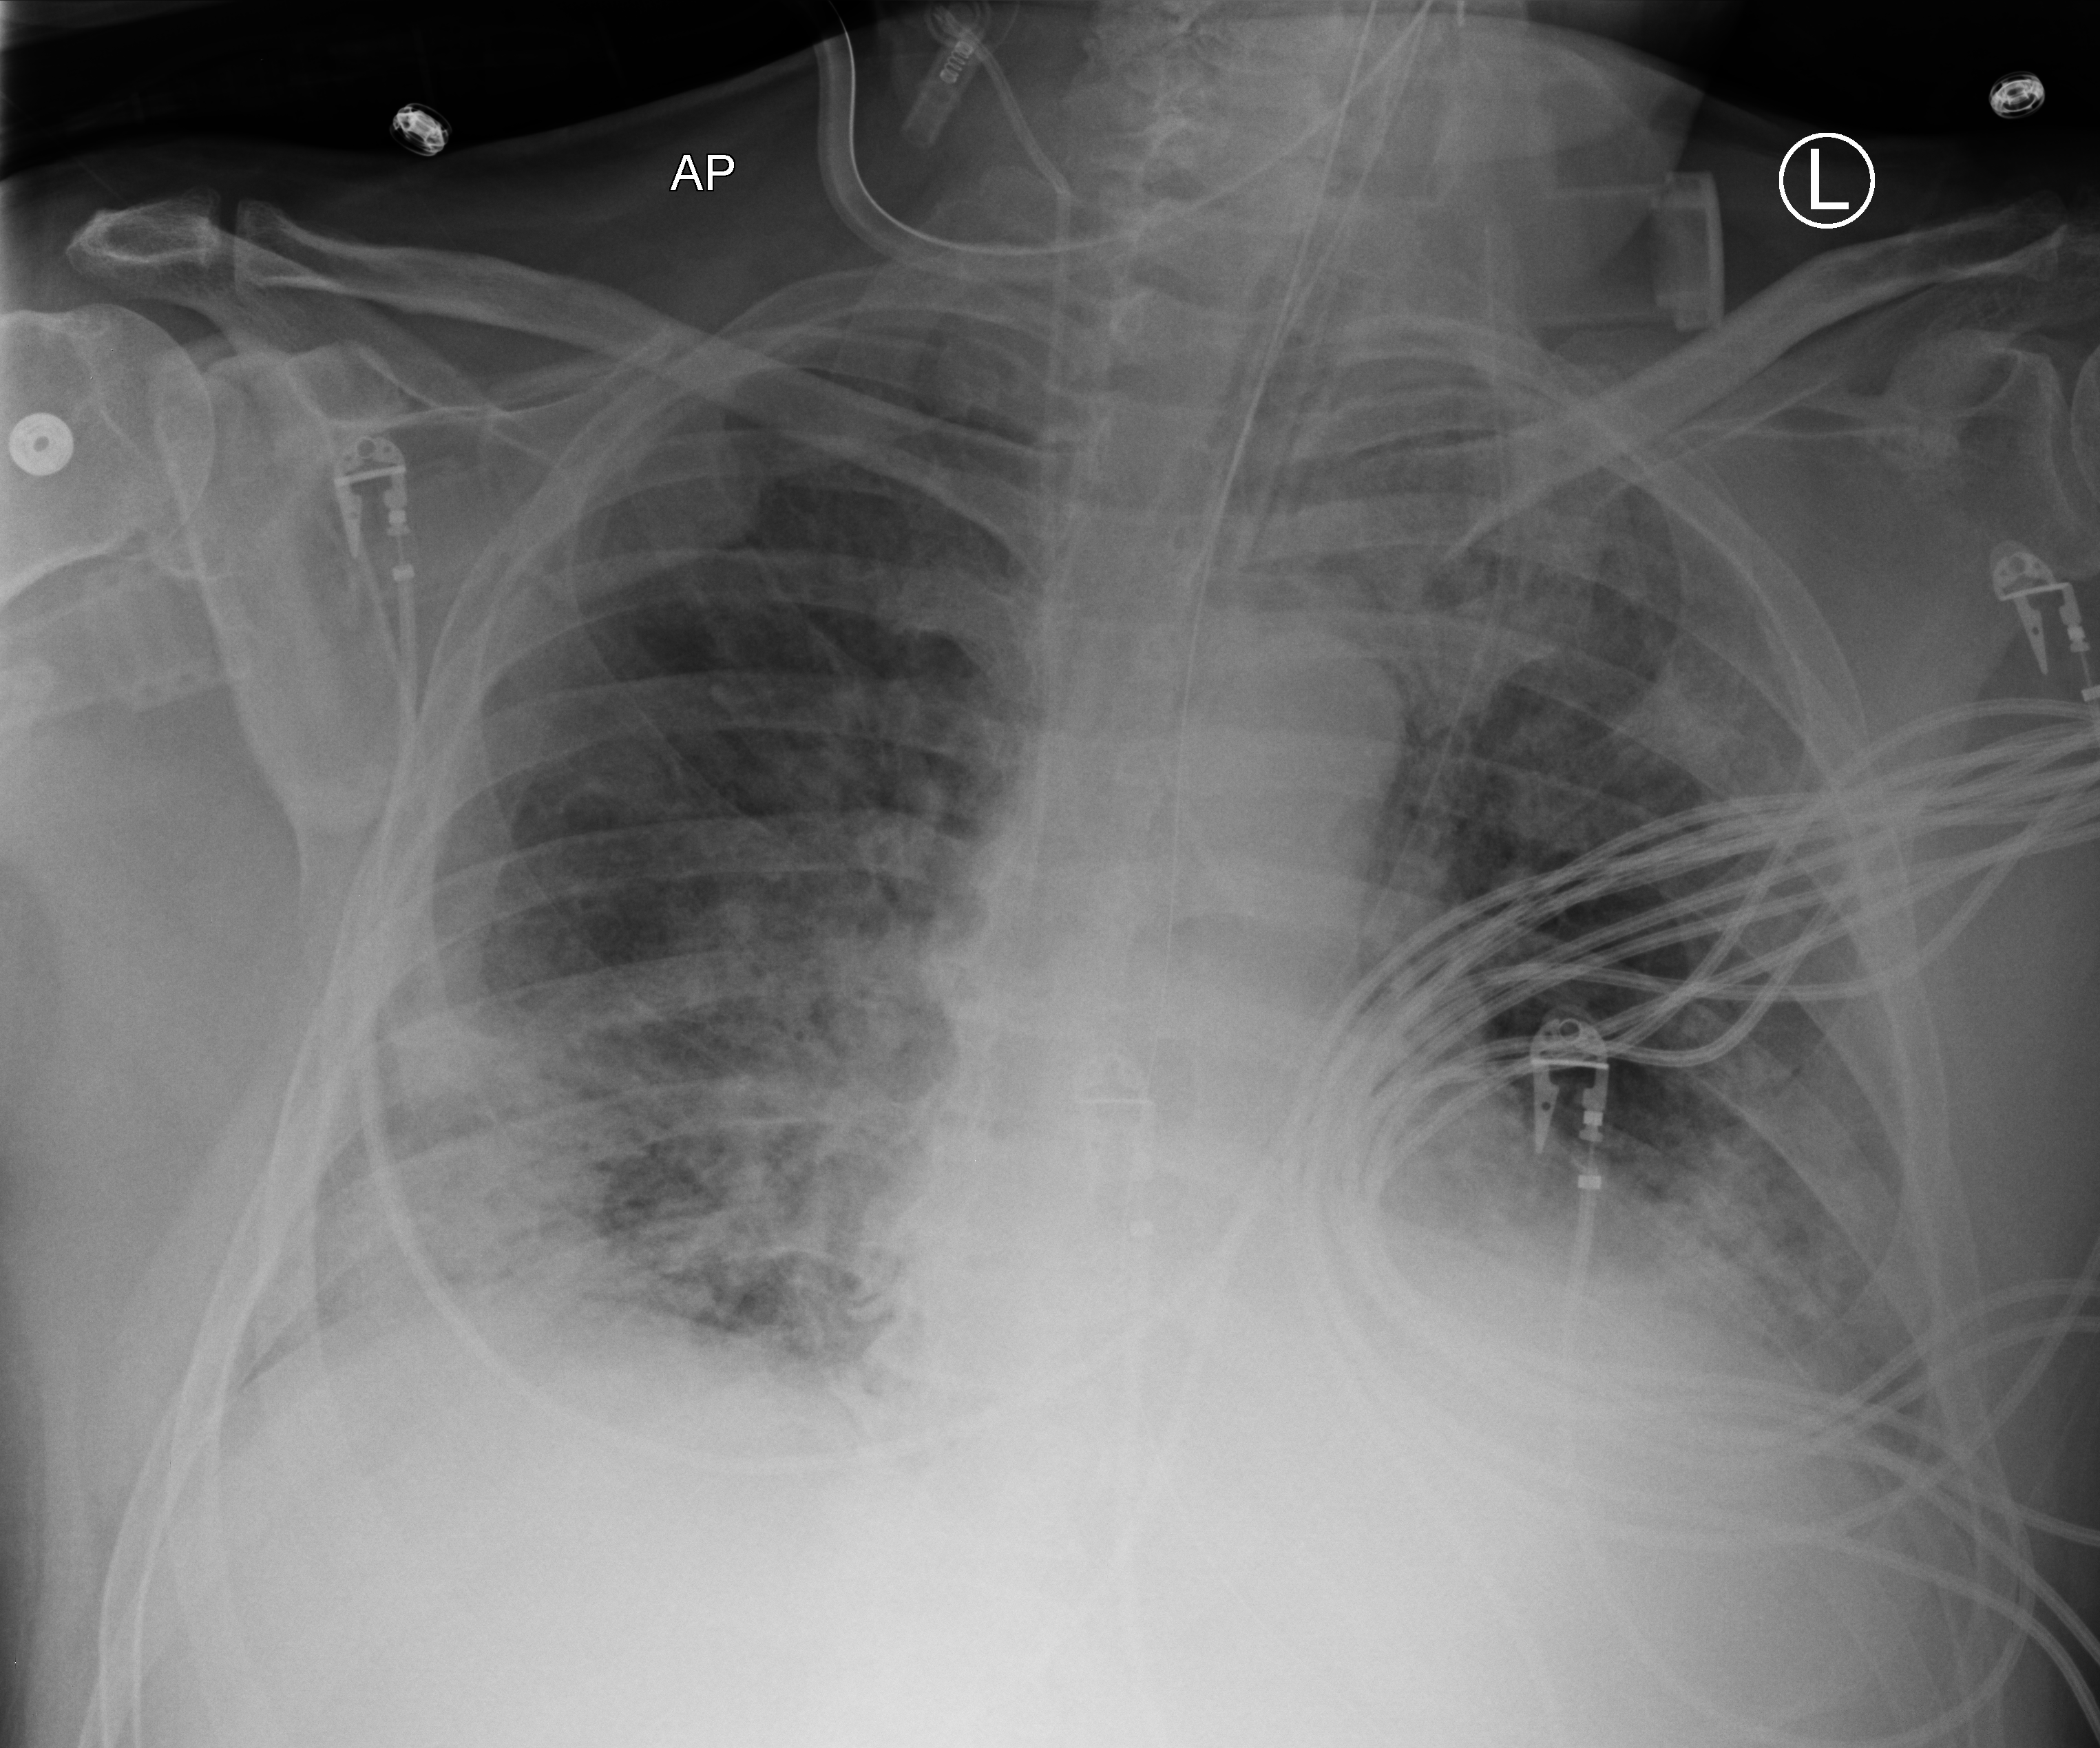
Chest X-ray (portable); anteroposterior (AP) projection. Patient hospitalised with COVID-19; male, aged 60–74 years.
Admission-level facts for this patient (not findings on this image; timing relative to this image not recorded): chronic kidney disease (admission record): no.